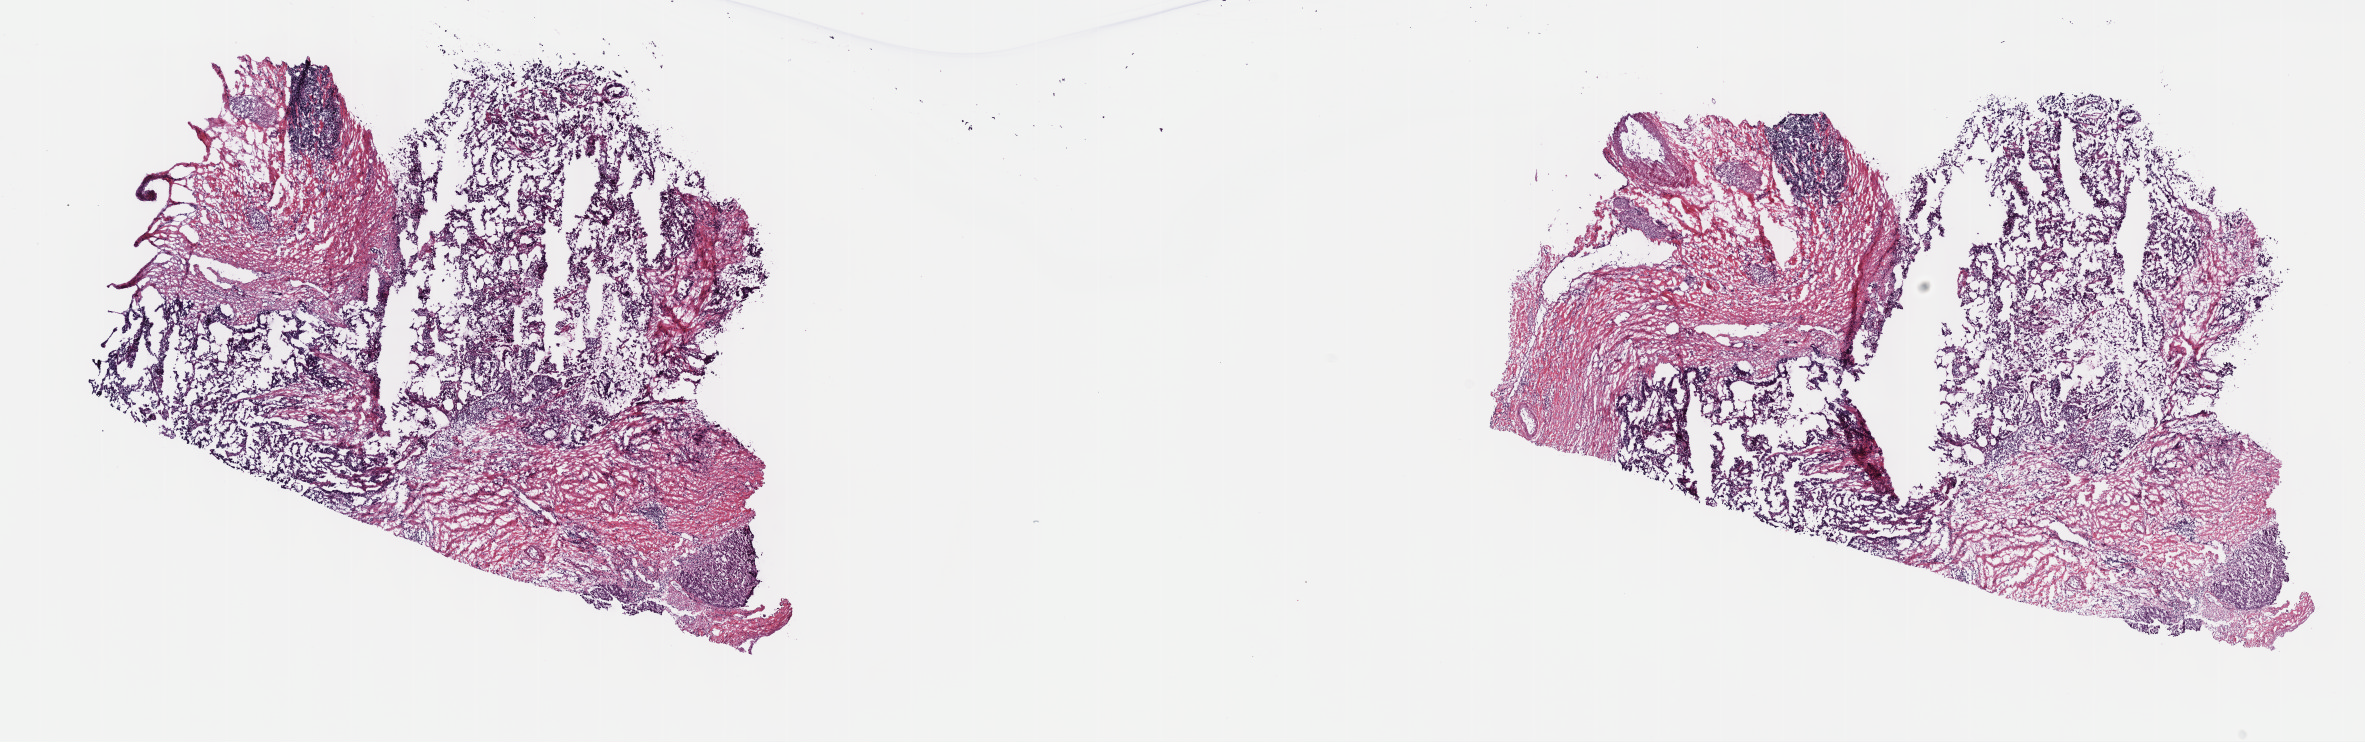
Whole-slide histology image, H&E — shown as a low-resolution overview of the whole scanned area (about 19.1 x 6.0 mm), frozen section from the top of the tissue portion, sample: primary tumour, bile duct. Female, age 66 years at initial diagnosis. Histologic grade: G2 (moderately differentiated). Slide review estimates, as recorded: tumour cells 65%, tumour nuclei 65%, normal cells 0%, stromal cells 35%, necrosis 0%. Infiltration values recorded for this section: lymphocyte infiltration 8%, monocyte infiltration 1%, neutrophil infiltration 3%.
AJCC pathologic stage: IVA (7th edition). Pathologic diagnosis: Cholangiocarcinoma (intrahepatic bile duct).